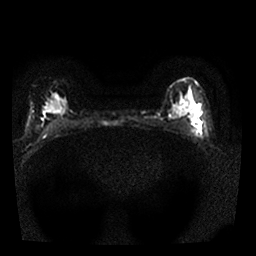
Breast MRI, one axial slice. Diffusion-weighted series; image 2 of 4 stored at this slice position (different b-values; order by instance number). 1.5 T. 4 mm slice thickness. 256 × 256 image matrix. Female patient.
Annotated regions visible in this slice (outlined manually by an expert reader):
- tumour on diffusion-weighted imaging: box from (x=191, y=118) to (x=195, y=124) px